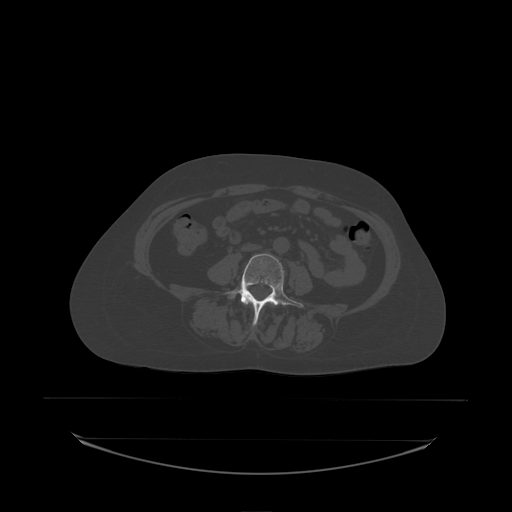
CT including the spine, one axial slice; slice 51 of 242 in the series (ordered by position); bone window (W 1800 / L 400 HU); 512 × 512 image matrix. Female patient, age 53 years. Case-level facts recorded for this patient, not image findings: primary cancer: lung.
Outlined on this slice (semi-automatic segmentation, software-assisted and operator-edited):
- L4 vertebra: box from (x=225, y=254) to (x=304, y=326) px